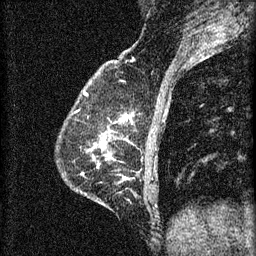
Breast MRI (dynamic contrast-enhanced), one sagittal slice; slice 19 of 60 in the series (ordered by position); 3 images stored at this slice position (order not interpretable as contrast timing); 1.5 T; TE 4.2 ms, TR 8.2 ms; 2 mm slice thickness; 256 × 256 image matrix, field of view 180 × 180 mm. Female patient, age 59 years.
Outlined on this slice (semi-automatically segmented with operator editing):
- analysis volume of interest (the breast-tissue region the enhancement analysis was run in; not a lesion): bounding box <72,112,134,161> (left, top, right, bottom; pixels)
- tumour enhancement mask (voxels above the 70 % enhancement threshold inside the analysis volume of interest): <120,118,127,121>